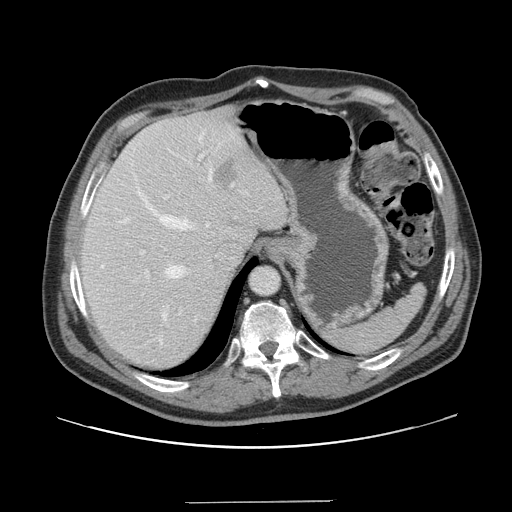
Contrast-enhanced abdominal CT, one axial slice; position 118 of 151 along the scan axis; 120 kVp; intravenous contrast given; soft-tissue window (W 400 / L 40 HU); 2.5 mm slice thickness; 512 × 512 image matrix, field of view 399 × 399 mm. Male patient, age 63 years. Case-level facts recorded for this patient, not image findings: diagnosis: colorectal cancer liver metastases, imaged before liver resection.
Outlined on this slice (expert manual segmentation):
- hepatic veins: bounding box (x1, y1, x2, y2) in pixels: (101, 133, 212, 319)
- liver: (79, 108, 287, 370)
- planned liver remnant (the part of the liver to remain after resection): (80, 117, 258, 370)
- portal vein (with intrahepatic branches): (140, 154, 233, 278)
- liver metastasis: (215, 158, 236, 188)